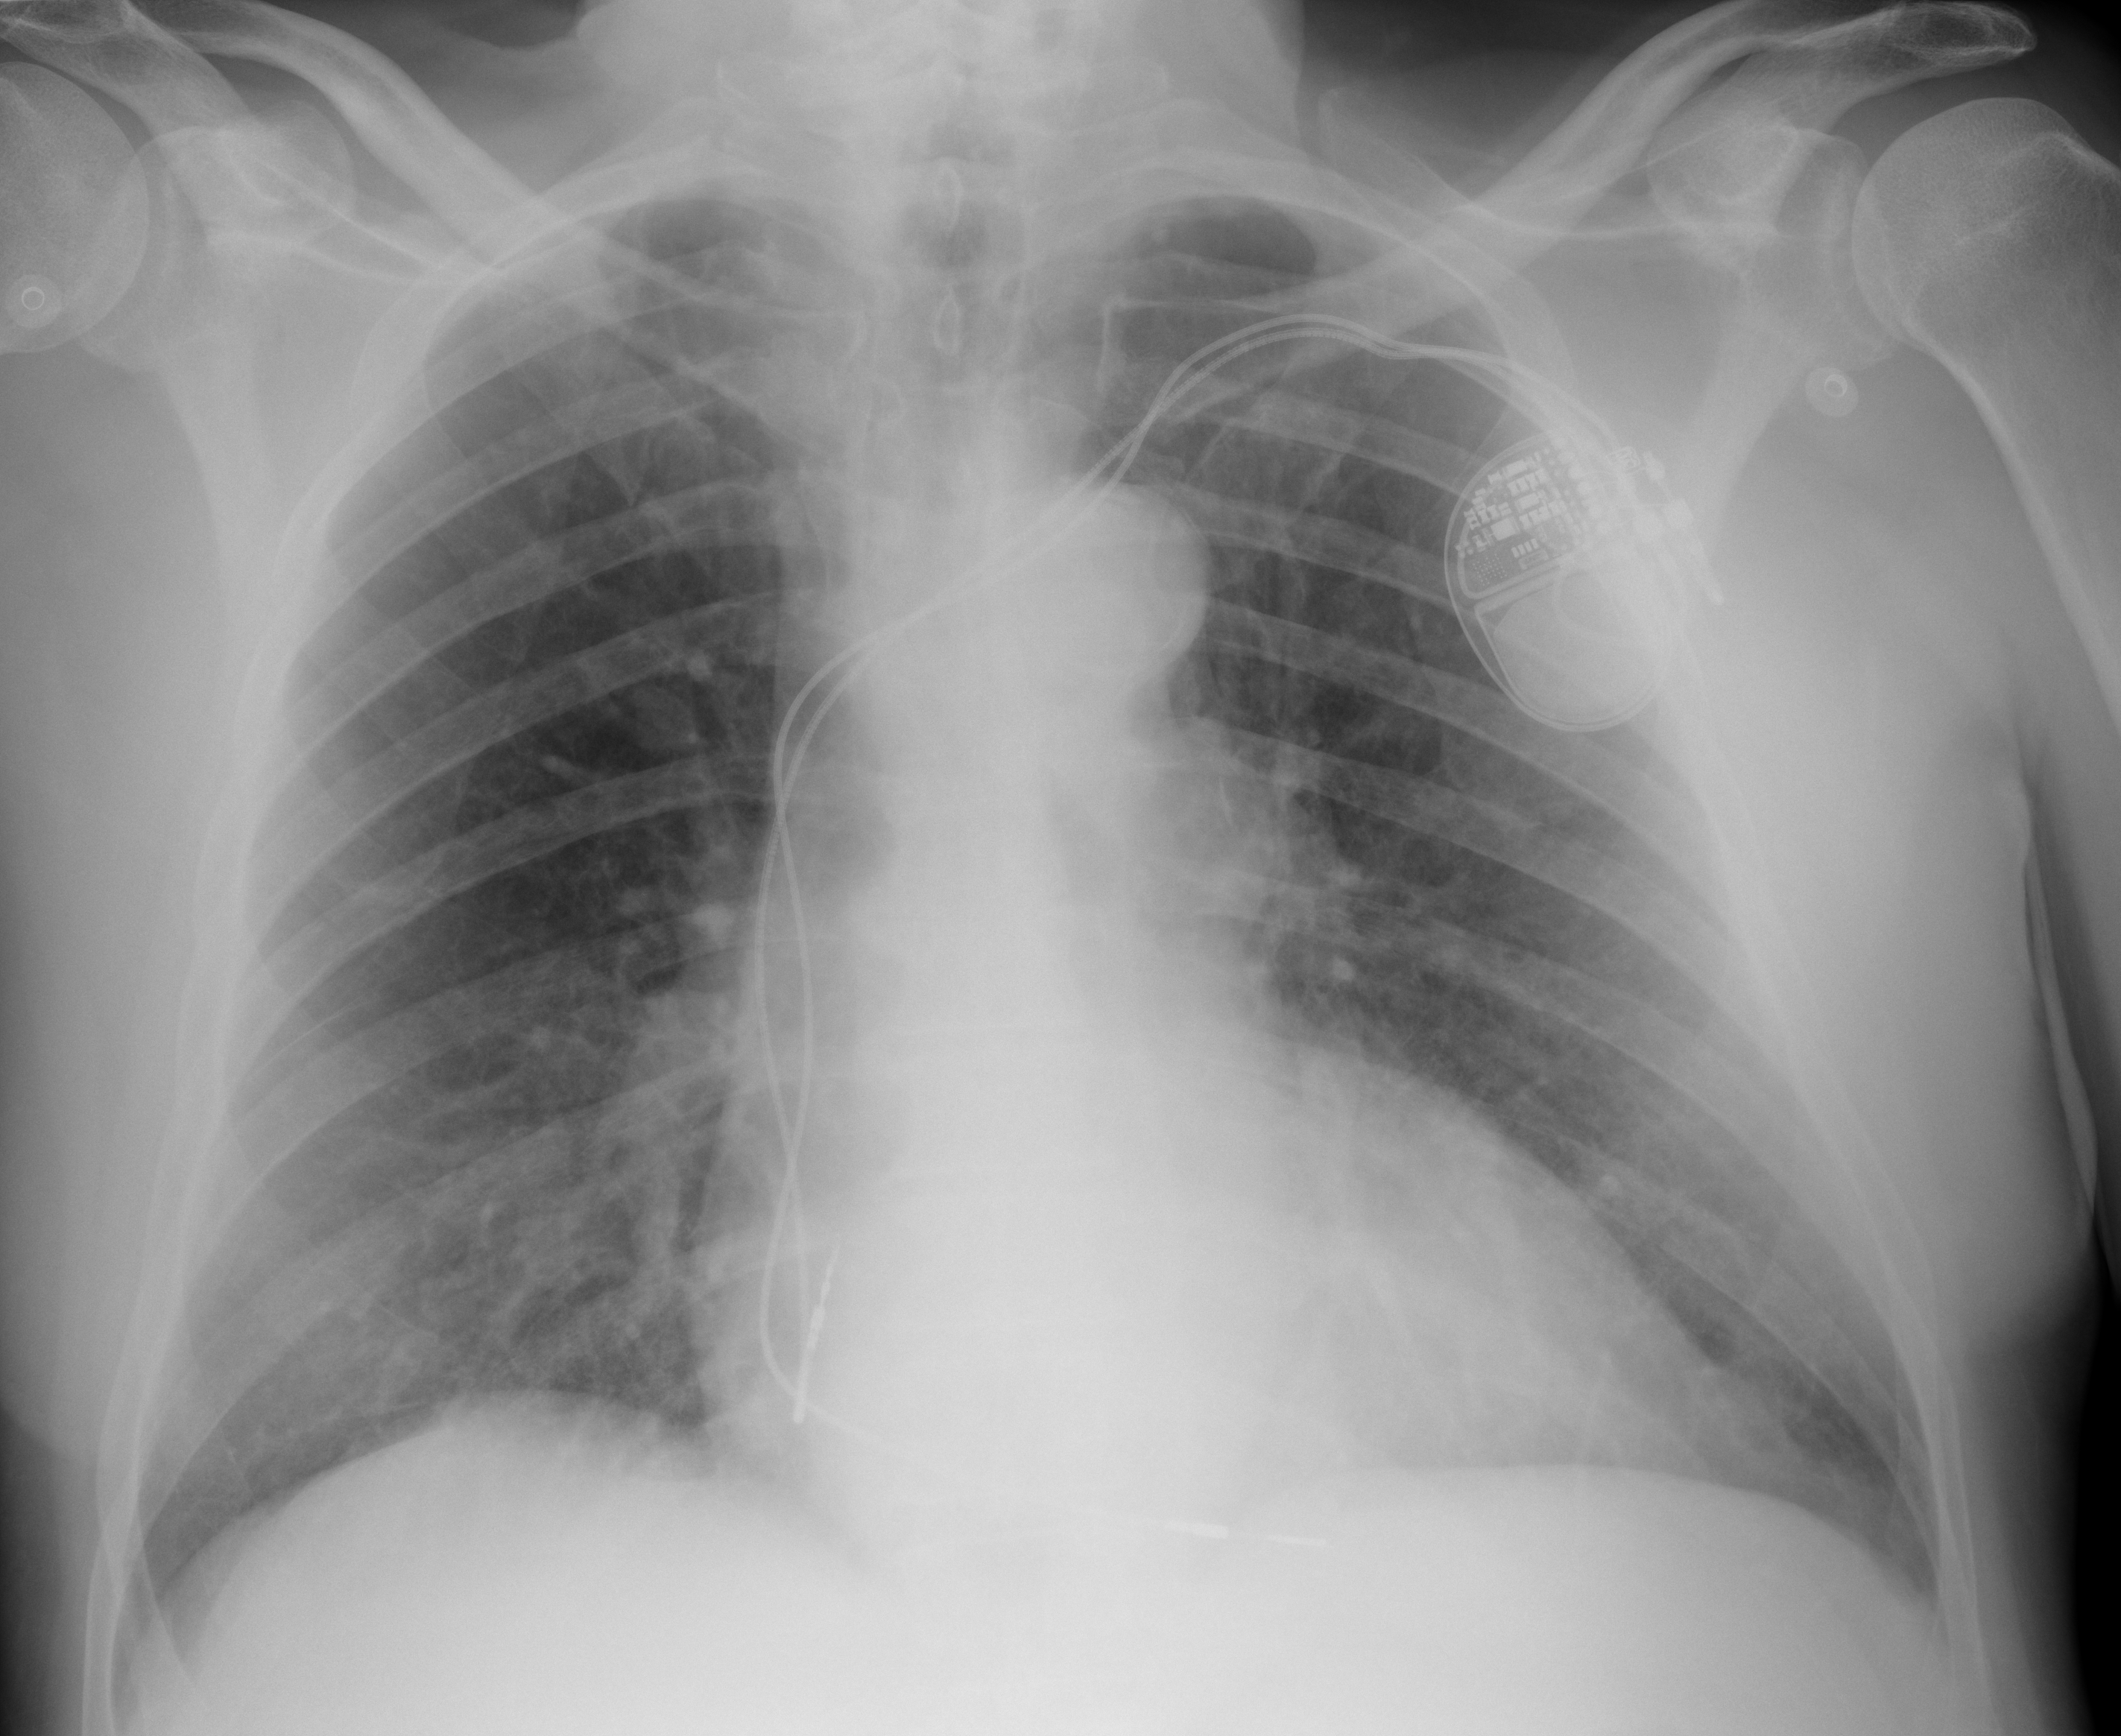
Portable chest radiograph, AP projection. Male patient, age 79 years; imaged 18 days after the COVID-19 diagnosis.
Radiologist key findings (as recorded): Trace right basilar opacity felt to represent atelectatic changes.